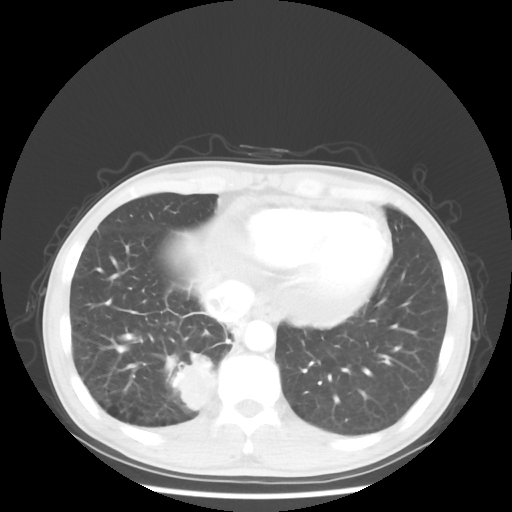
Chest CT, one axial slice. Slice 12 of 58 in the series (ordered by position). Reconstruction kernel STANDARD. 100 kVp. Lung window (W 1500 / L -600 HU). 512 × 512 image matrix. Patient: male, 56 years. From the clinical record (not read from this slice): clinical TNM (as recorded): T2 N1 M1; histopathological grade: G1.
Structures marked on this image (bounding box drawn by a radiologist):
- lung tumour (recorded histology: adenocarcinoma): bounding box (x1, y1, x2, y2) in pixels: (170, 349, 218, 415)